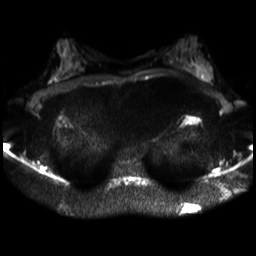
Breast MRI, one axial slice; slice 16 of 30 in the series (ordered by position); diffusion-weighted series; image 2 of 4 stored at this slice position (different b-values; order by instance number); 3 T; 4 mm slice thickness; 256 × 256 image matrix, field of view 320 × 320 mm. Female patient.
Annotated regions visible in this slice (outlined manually by an expert reader):
- tumour on diffusion-weighted imaging: bounding box <198,66,205,79> (left, top, right, bottom; pixels)